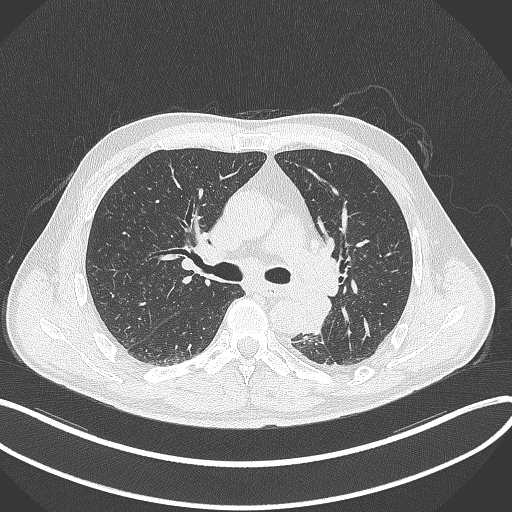
Chest CT, one axial slice; slice 212 of 329 in the series (ordered by position); 120 kVp; lung window (W 1500 / L -600 HU); 1 mm slice thickness; 512 × 512 image matrix, field of view 400 × 400 mm. Patient: male, 59 years. From the clinical record (not read from this slice): clinical TNM (as recorded): T2a N2 M0.
Structures marked on this image (bounding box drawn by a radiologist):
- lung tumour (recorded histology: squamous cell carcinoma): bounding box (x1, y1, x2, y2) in pixels: (302, 289, 335, 336)